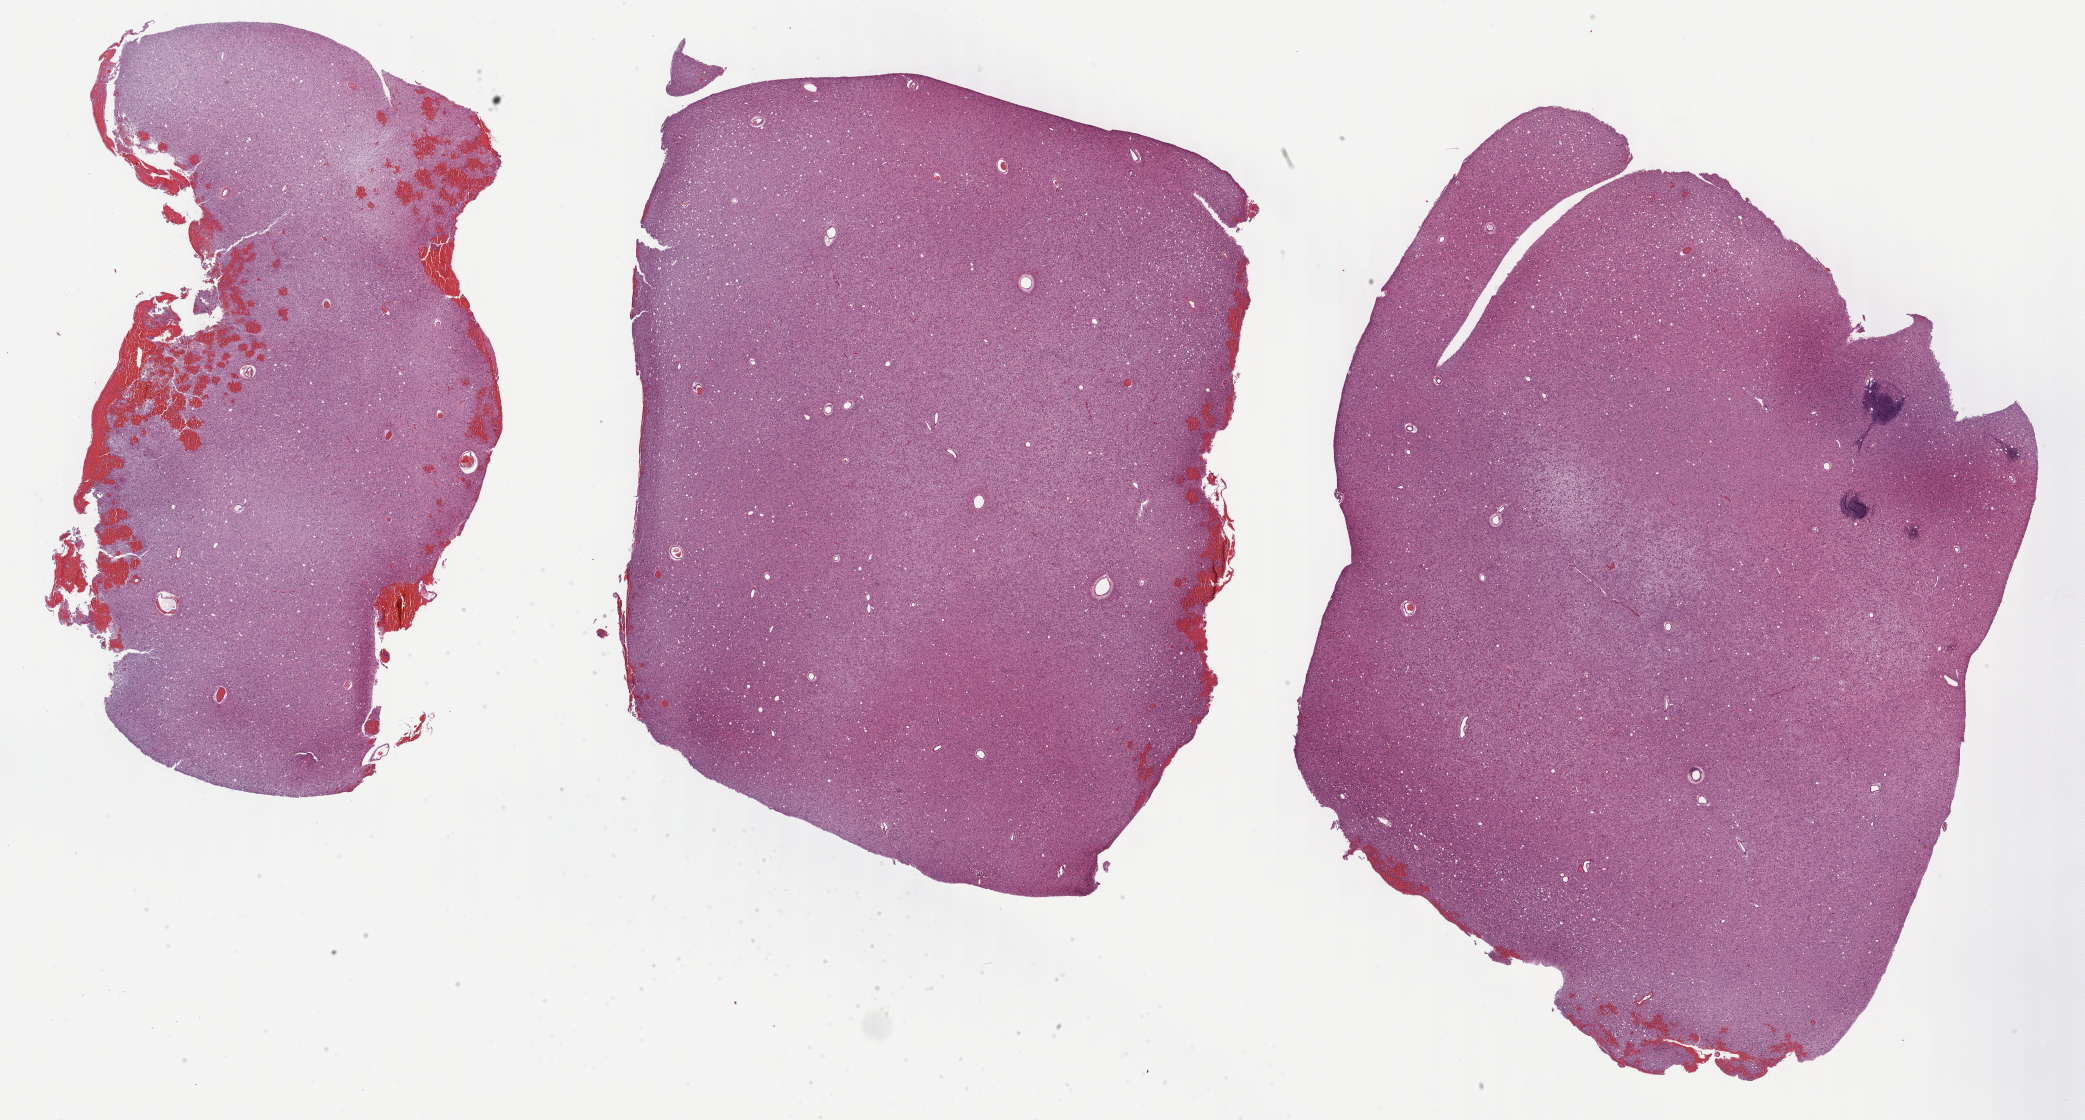
H&E-stained whole-slide image — whole scanned area (about 33.7 x 18.1 mm, from a 40x scan) shown as a low-resolution overview, formalin-fixed paraffin-embedded (FFPE) diagnostic section, primary tumour sample from the brain. Female, age 24 years at initial diagnosis. Histologic grade: G2 (moderately differentiated).
Histologic diagnosis: Astrocytoma, NOS (cerebrum).